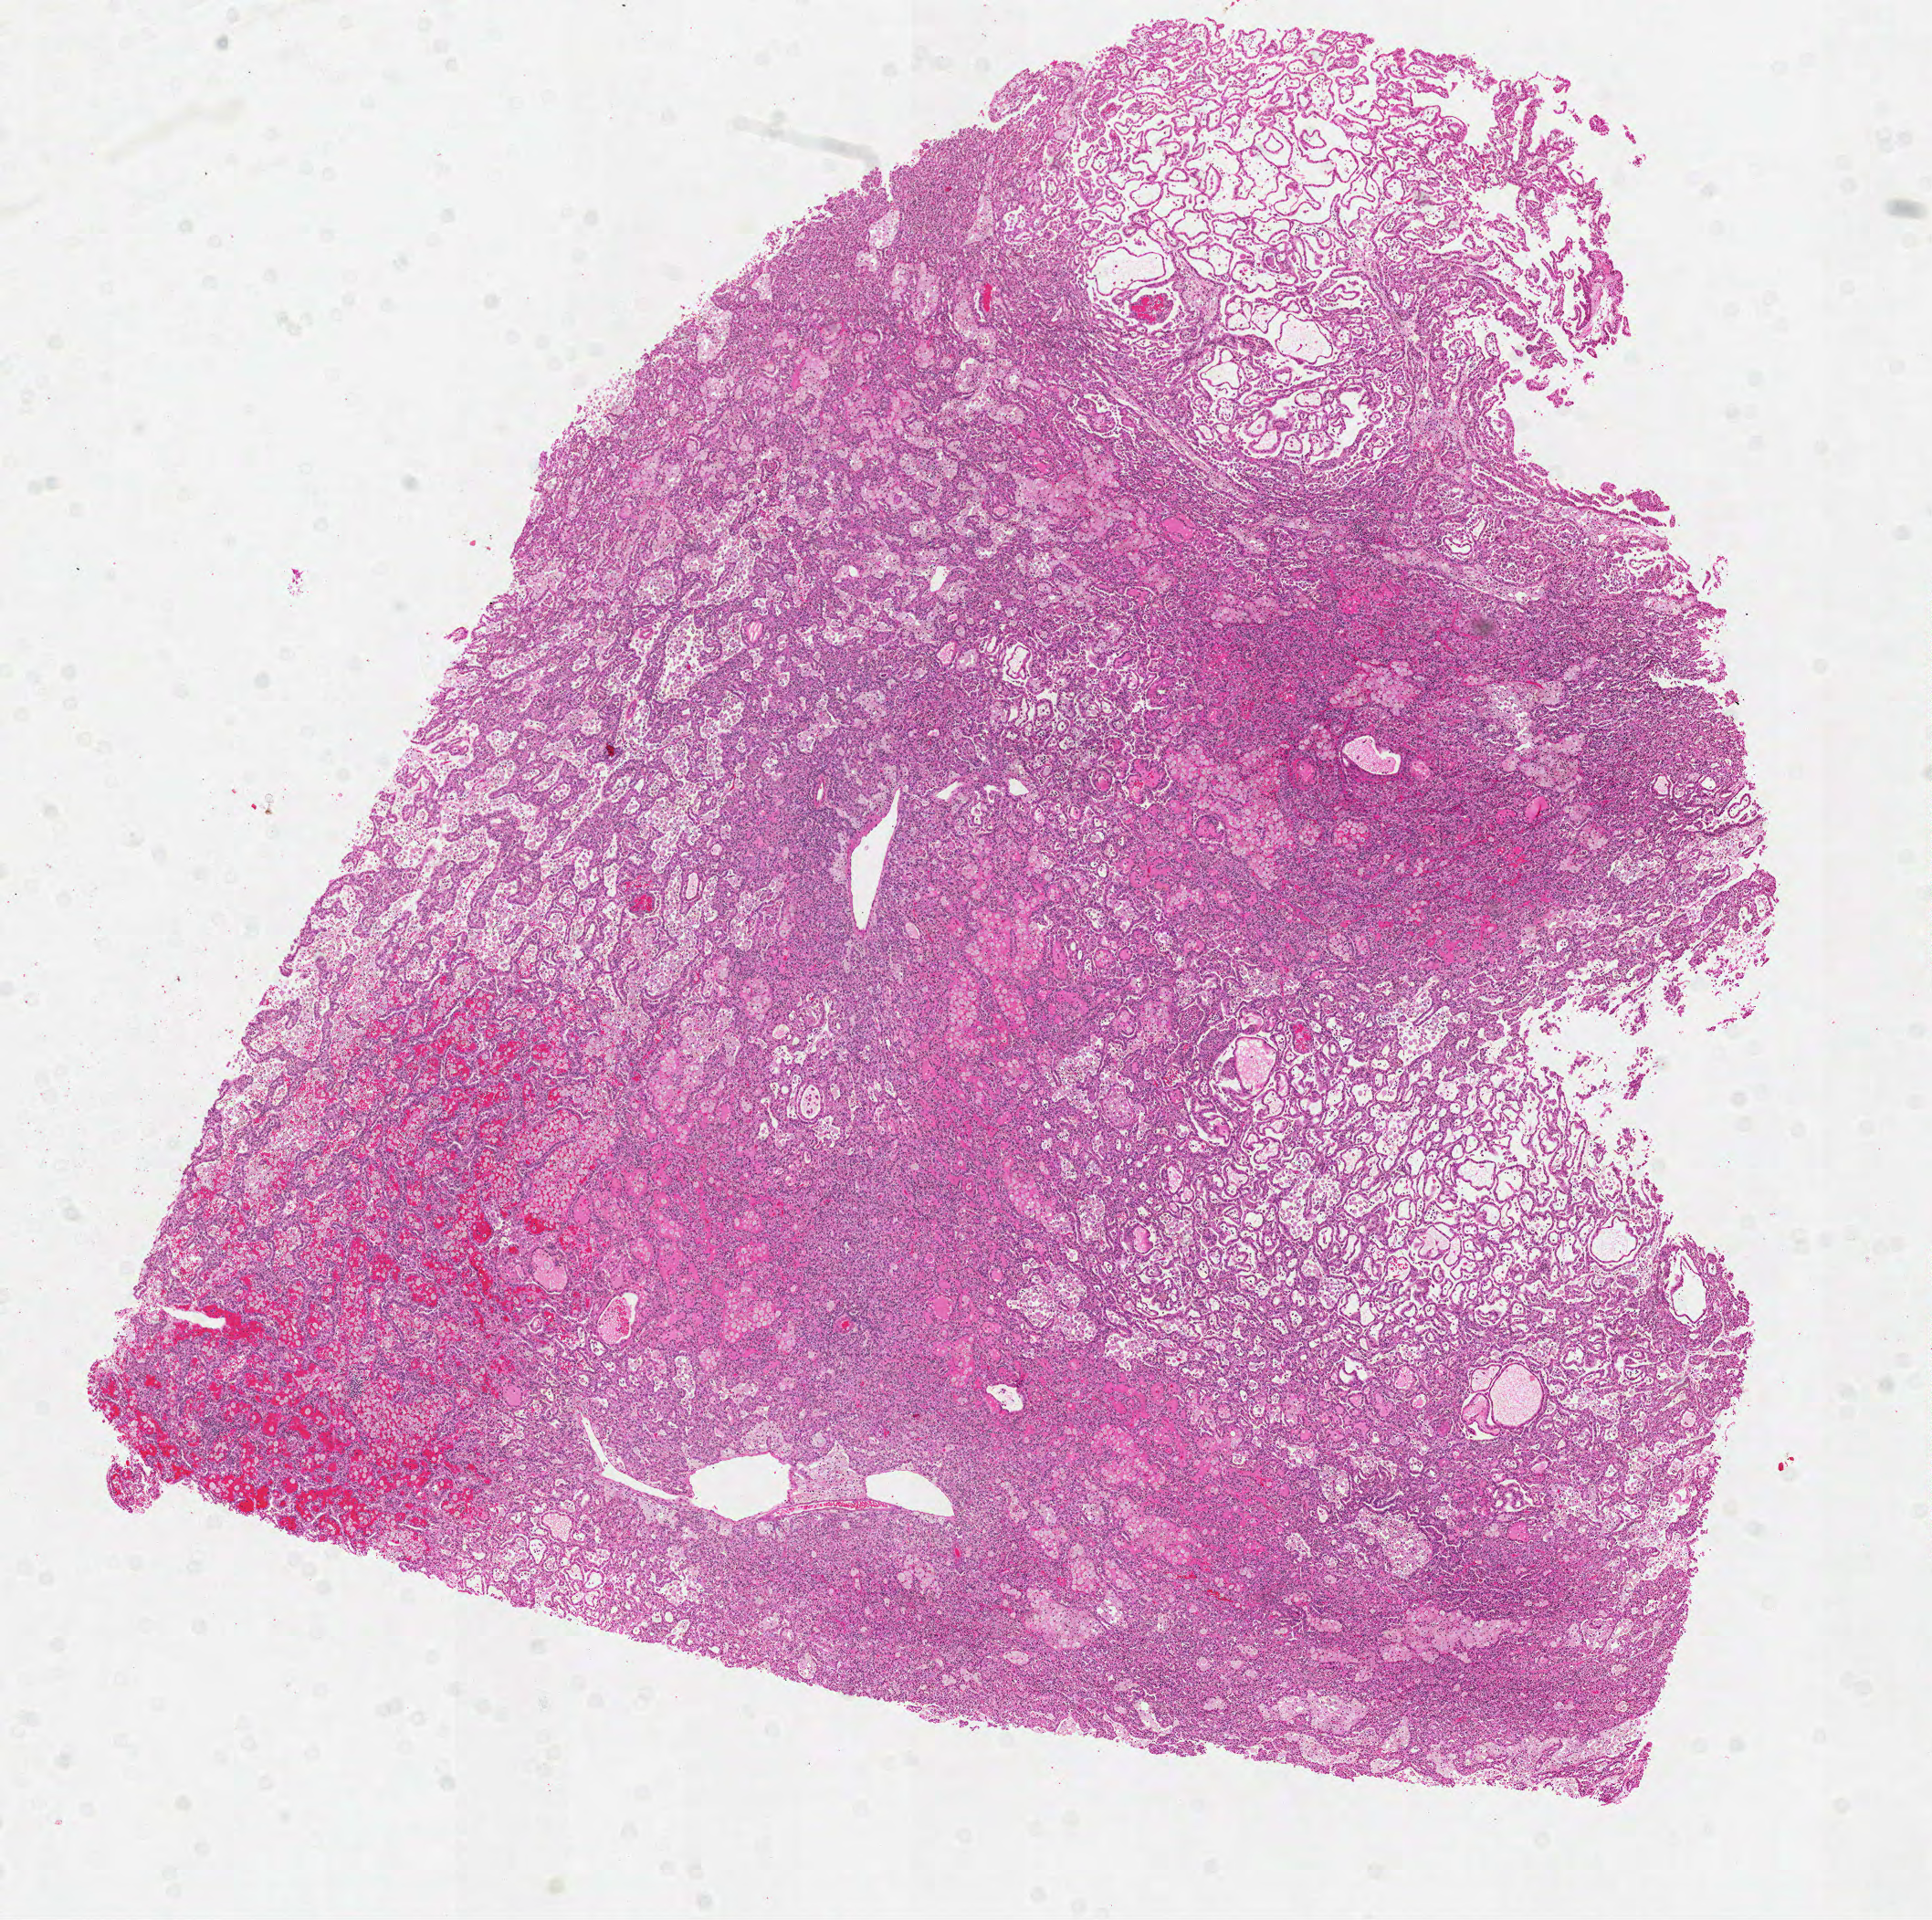
H&E-stained whole-slide image — whole scanned area (about 8.5 x 8.5 mm) shown as a low-resolution overview; FFPE section; kidney, primary tumour sample. Male patient; age at initial diagnosis 64 years.
AJCC pathologic stage: I (5th edition). Pathologic diagnosis: Papillary adenocarcinoma, NOS.